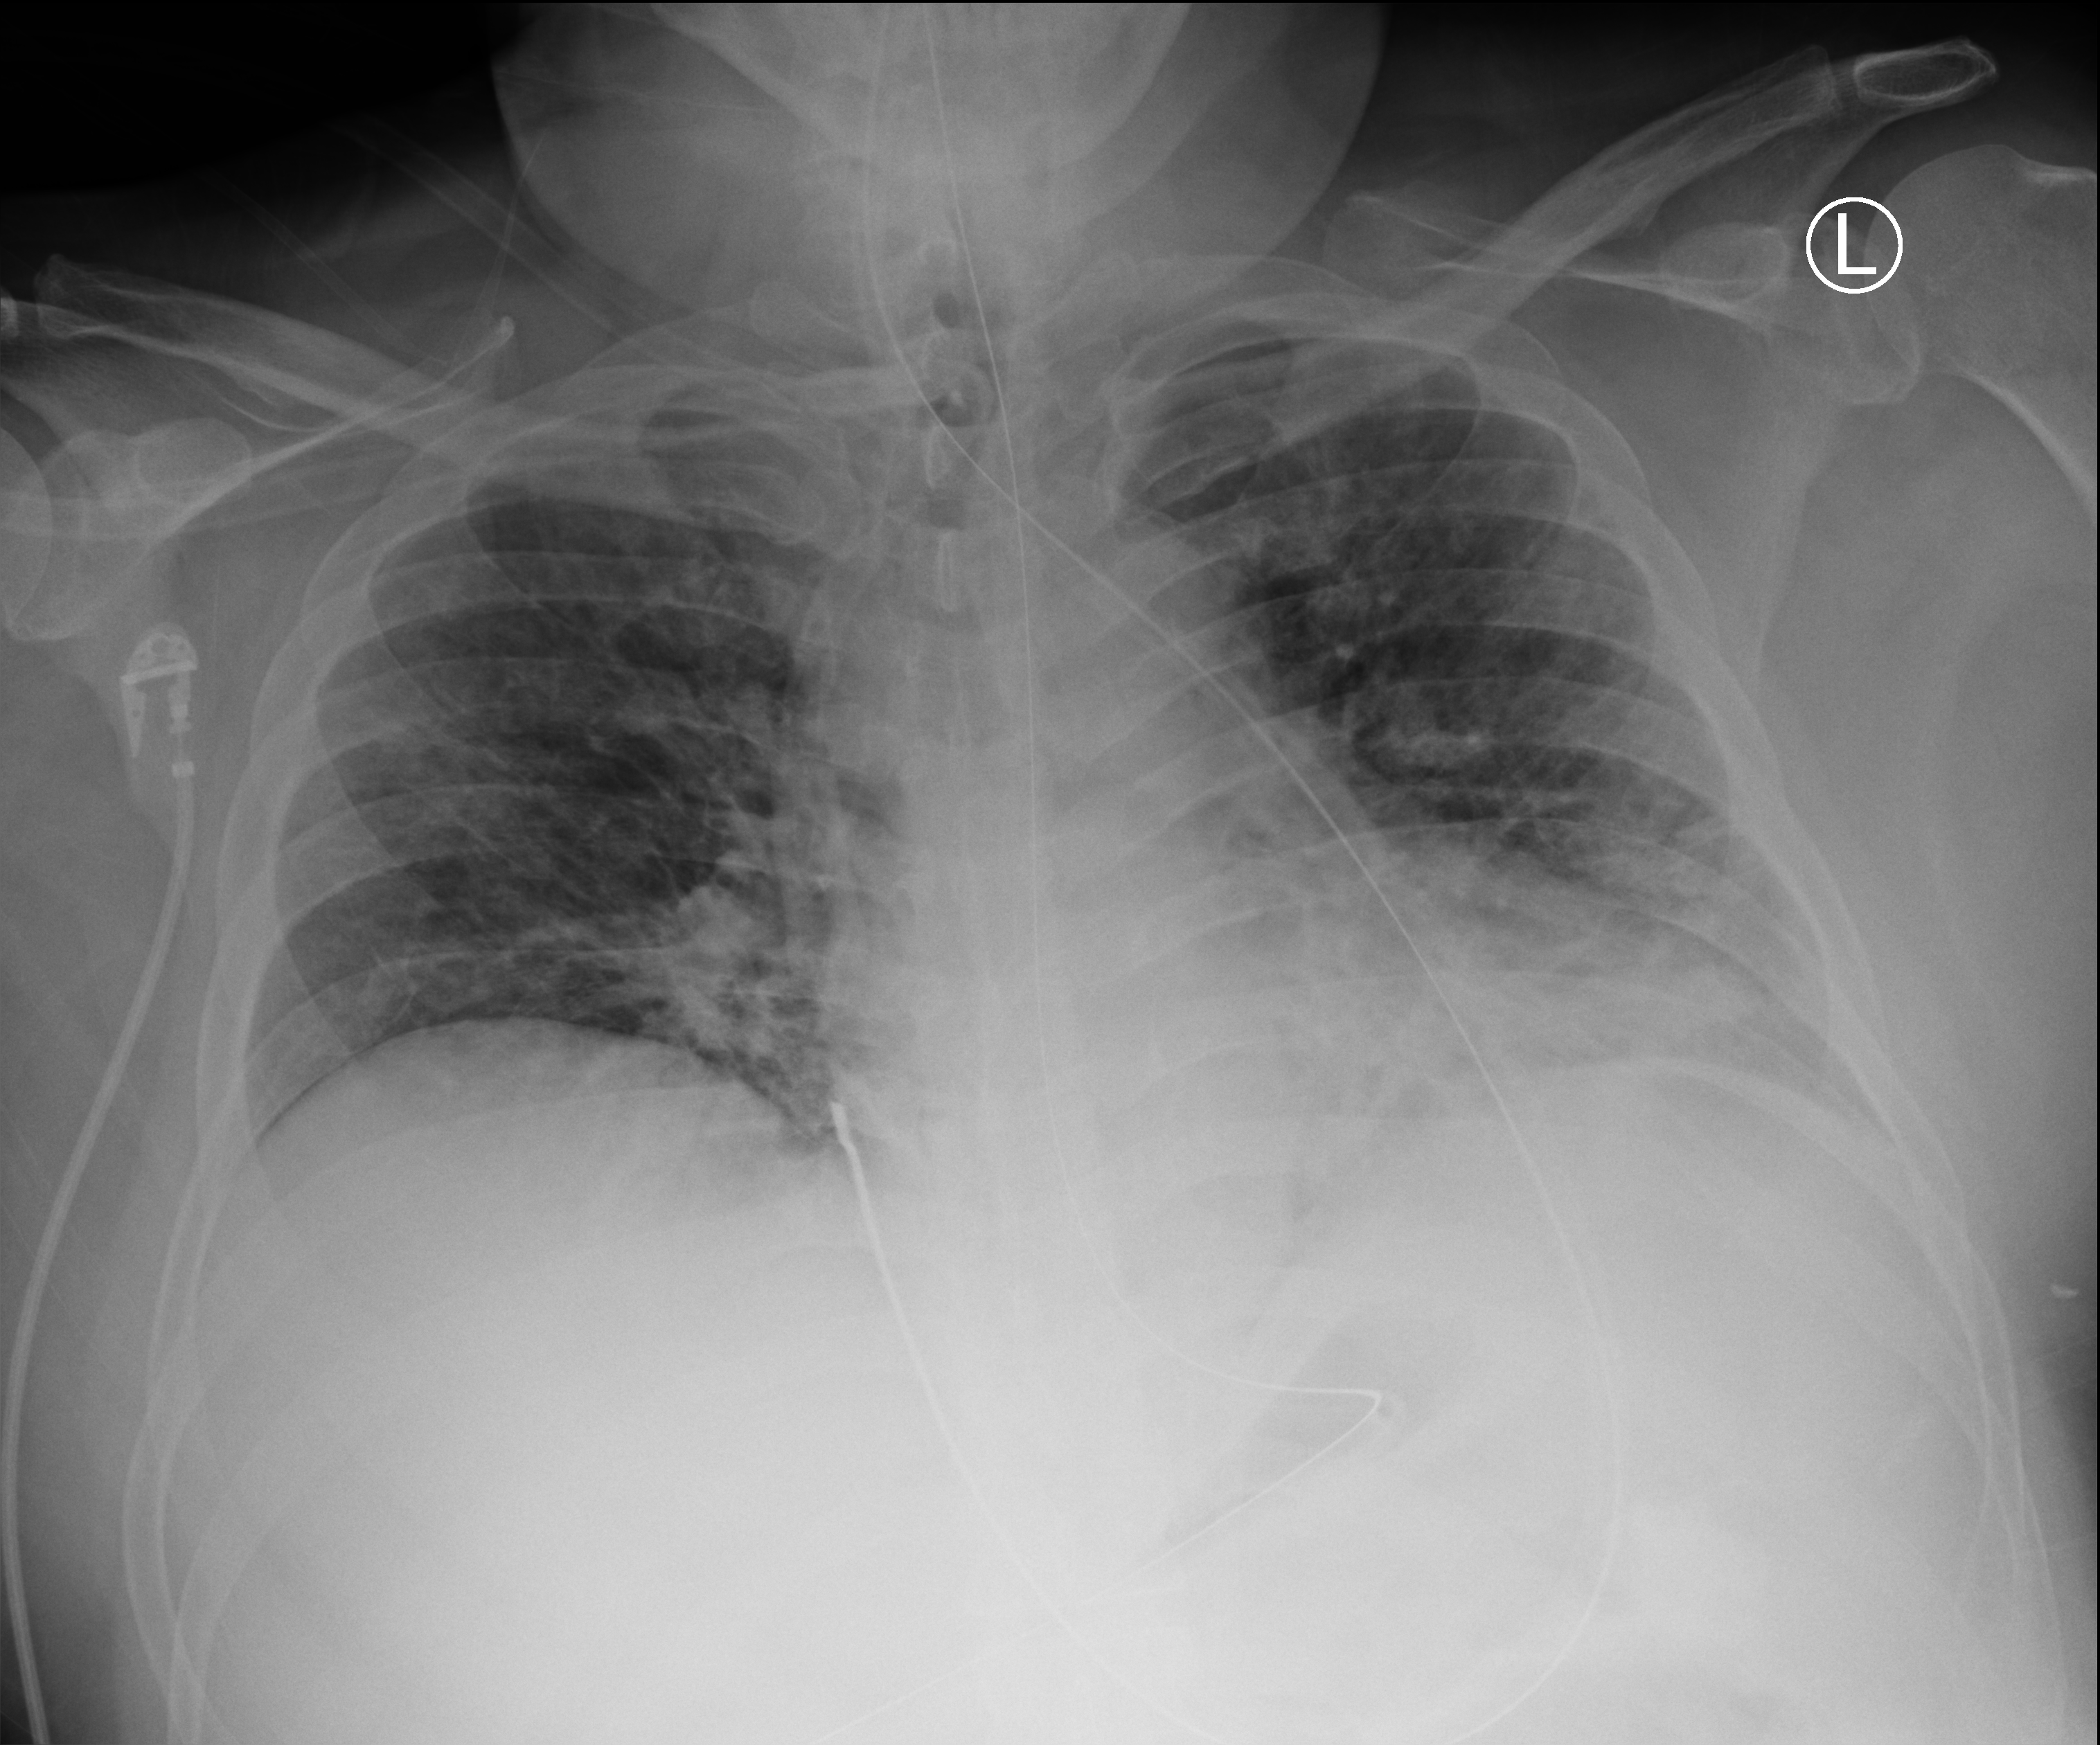
Portable chest radiograph, anteroposterior (AP) projection. Male patient hospitalised with COVID-19, age 18–59 years.
From the hospital-stay record, not from the radiograph (when in the stay this image was taken is not recorded): mechanically ventilated during this hospital stay: no.